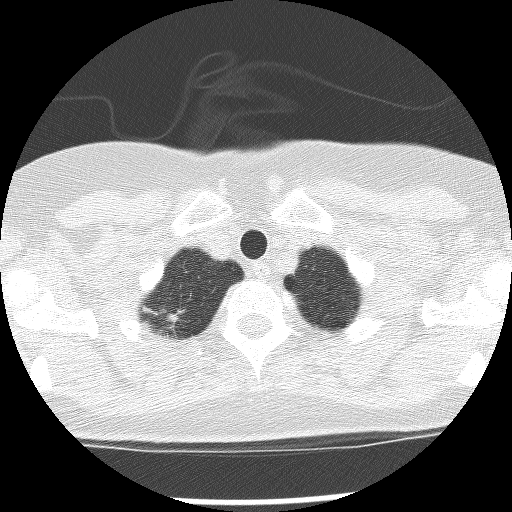
Chest CT (low-dose screening protocol), one axial image; baseline screening round; lung window (W 1500 / L -600 HU). Female participant, aged 56 years at enrolment. Current smoker at enrolment.
Lesion marked by an expert reader, box from (x=140, y=297) to (x=199, y=341) px. Screening reader's record for this exam: no non-calcified nodule ≥4 mm recorded. Participant outcome: lung cancer diagnosed 729 days after this screen (after the third annual screen) — large cell carcinoma, NOS, right upper lobe, poorly differentiated (G3), stage IB (AJCC 6th edition), 15 mm at pathology.